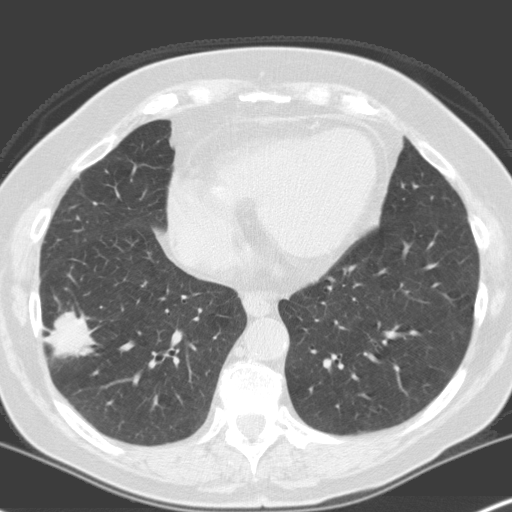
Axial slice from a low-dose chest CT screening exam. Baseline screening round. Lung window (W 1500 / L -600 HU). 3.2 mm slice thickness. Standard (soft-tissue) reconstruction kernel (C). 512 × 512 image matrix. Female participant, aged 70 years at enrolment. Current smoker at enrolment.
Expert-annotated lung lesion, bounding box [x1, y1, x2, y2] px = [32, 300, 100, 369]. The screening reader recorded 4 non-calcified nodules or masses ≥4 mm on this exam (right lower lobe, right upper lobe, left upper lobe, left upper lobe); which of them this box marks is not recorded. Official screen result: positive, change unspecified: nodule(s) >= 4 mm or enlarging nodule(s), mass(es), or other non-specific abnormalities suspicious for lung cancer.